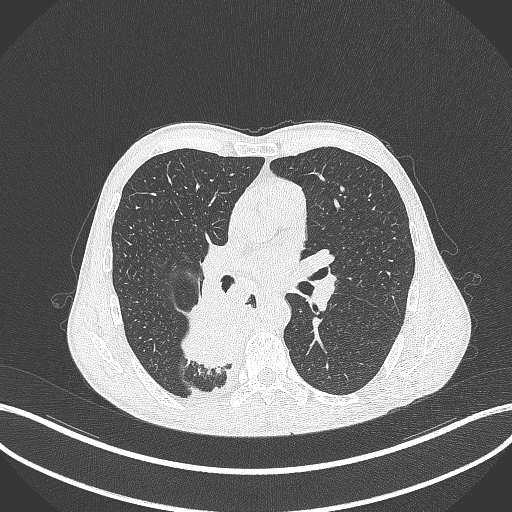
Chest CT, one axial slice; slice 206 of 371 in the series (ordered by position); 120 kVp; lung window (W 1500 / L -600 HU); 1 mm slice thickness; 512 × 512 image matrix. Male patient, age 58 years. Case-level facts recorded for this patient, not image findings: clinical TNM (as recorded): T3 N1 M1.
Structures marked on this image (rectangle marked by the reading radiologist):
- lung tumour (recorded histology: squamous cell carcinoma): bounding box <173,290,252,368> (left, top, right, bottom; pixels)